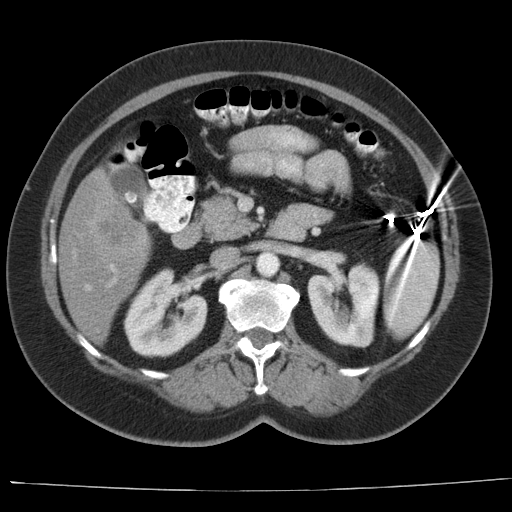
Contrast-enhanced abdominal CT, one axial slice; slice 12 of 44 in the series (ordered by position); reconstruction kernel AA-1; 140 kVp; intravenous contrast given; soft-tissue window (W 400 / L 40 HU); 5 mm slice thickness; 512 × 512 image matrix, field of view 373 × 373 mm. Female patient. Case-level facts recorded for this patient, not image findings: diagnosis: colorectal cancer liver metastases, imaged before liver resection; multiple liver metastases: yes; largest metastasis: 1.8 cm; disease in both lobes: no.
Structures marked on this image (manually delineated by an expert):
- hepatic veins: bounding box [x1, y1, x2, y2] px = [85, 285, 90, 291]
- liver: [61, 162, 150, 344]
- portal vein (with intrahepatic branches): [108, 265, 117, 286]
- liver metastasis: [83, 190, 102, 206]
- liver metastasis: [86, 204, 145, 258]